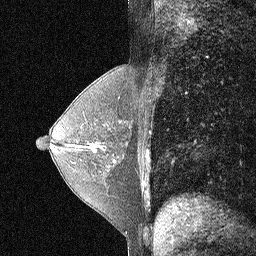
Breast MRI (dynamic contrast-enhanced), one sagittal slice; position 32 of 64 along the scan axis; dynamic contrast-enhanced study with each time point stored as its own series, time point 2 of 3 at this slice position (early post-contrast, ordered by acquisition time); 1.5 T; TE 4.5 ms, TR 11 ms; 2.06 mm slice thickness; 256 × 256 image matrix. Female patient, age 55 years. Case-level facts recorded for this patient, not image findings: setting: breast cancer imaged before/during neoadjuvant chemotherapy; receptor status: HR-positive, HER2-negative.
Outlined on this slice (semi-automatically segmented with operator editing):
- analysis volume of interest (the breast-tissue region the enhancement analysis was run in; not a lesion): bounding box [x1, y1, x2, y2] px = [72, 110, 133, 190]
- tumour enhancement mask (voxels above the 90 % enhancement threshold inside the analysis volume of interest): [94, 150, 96, 152]